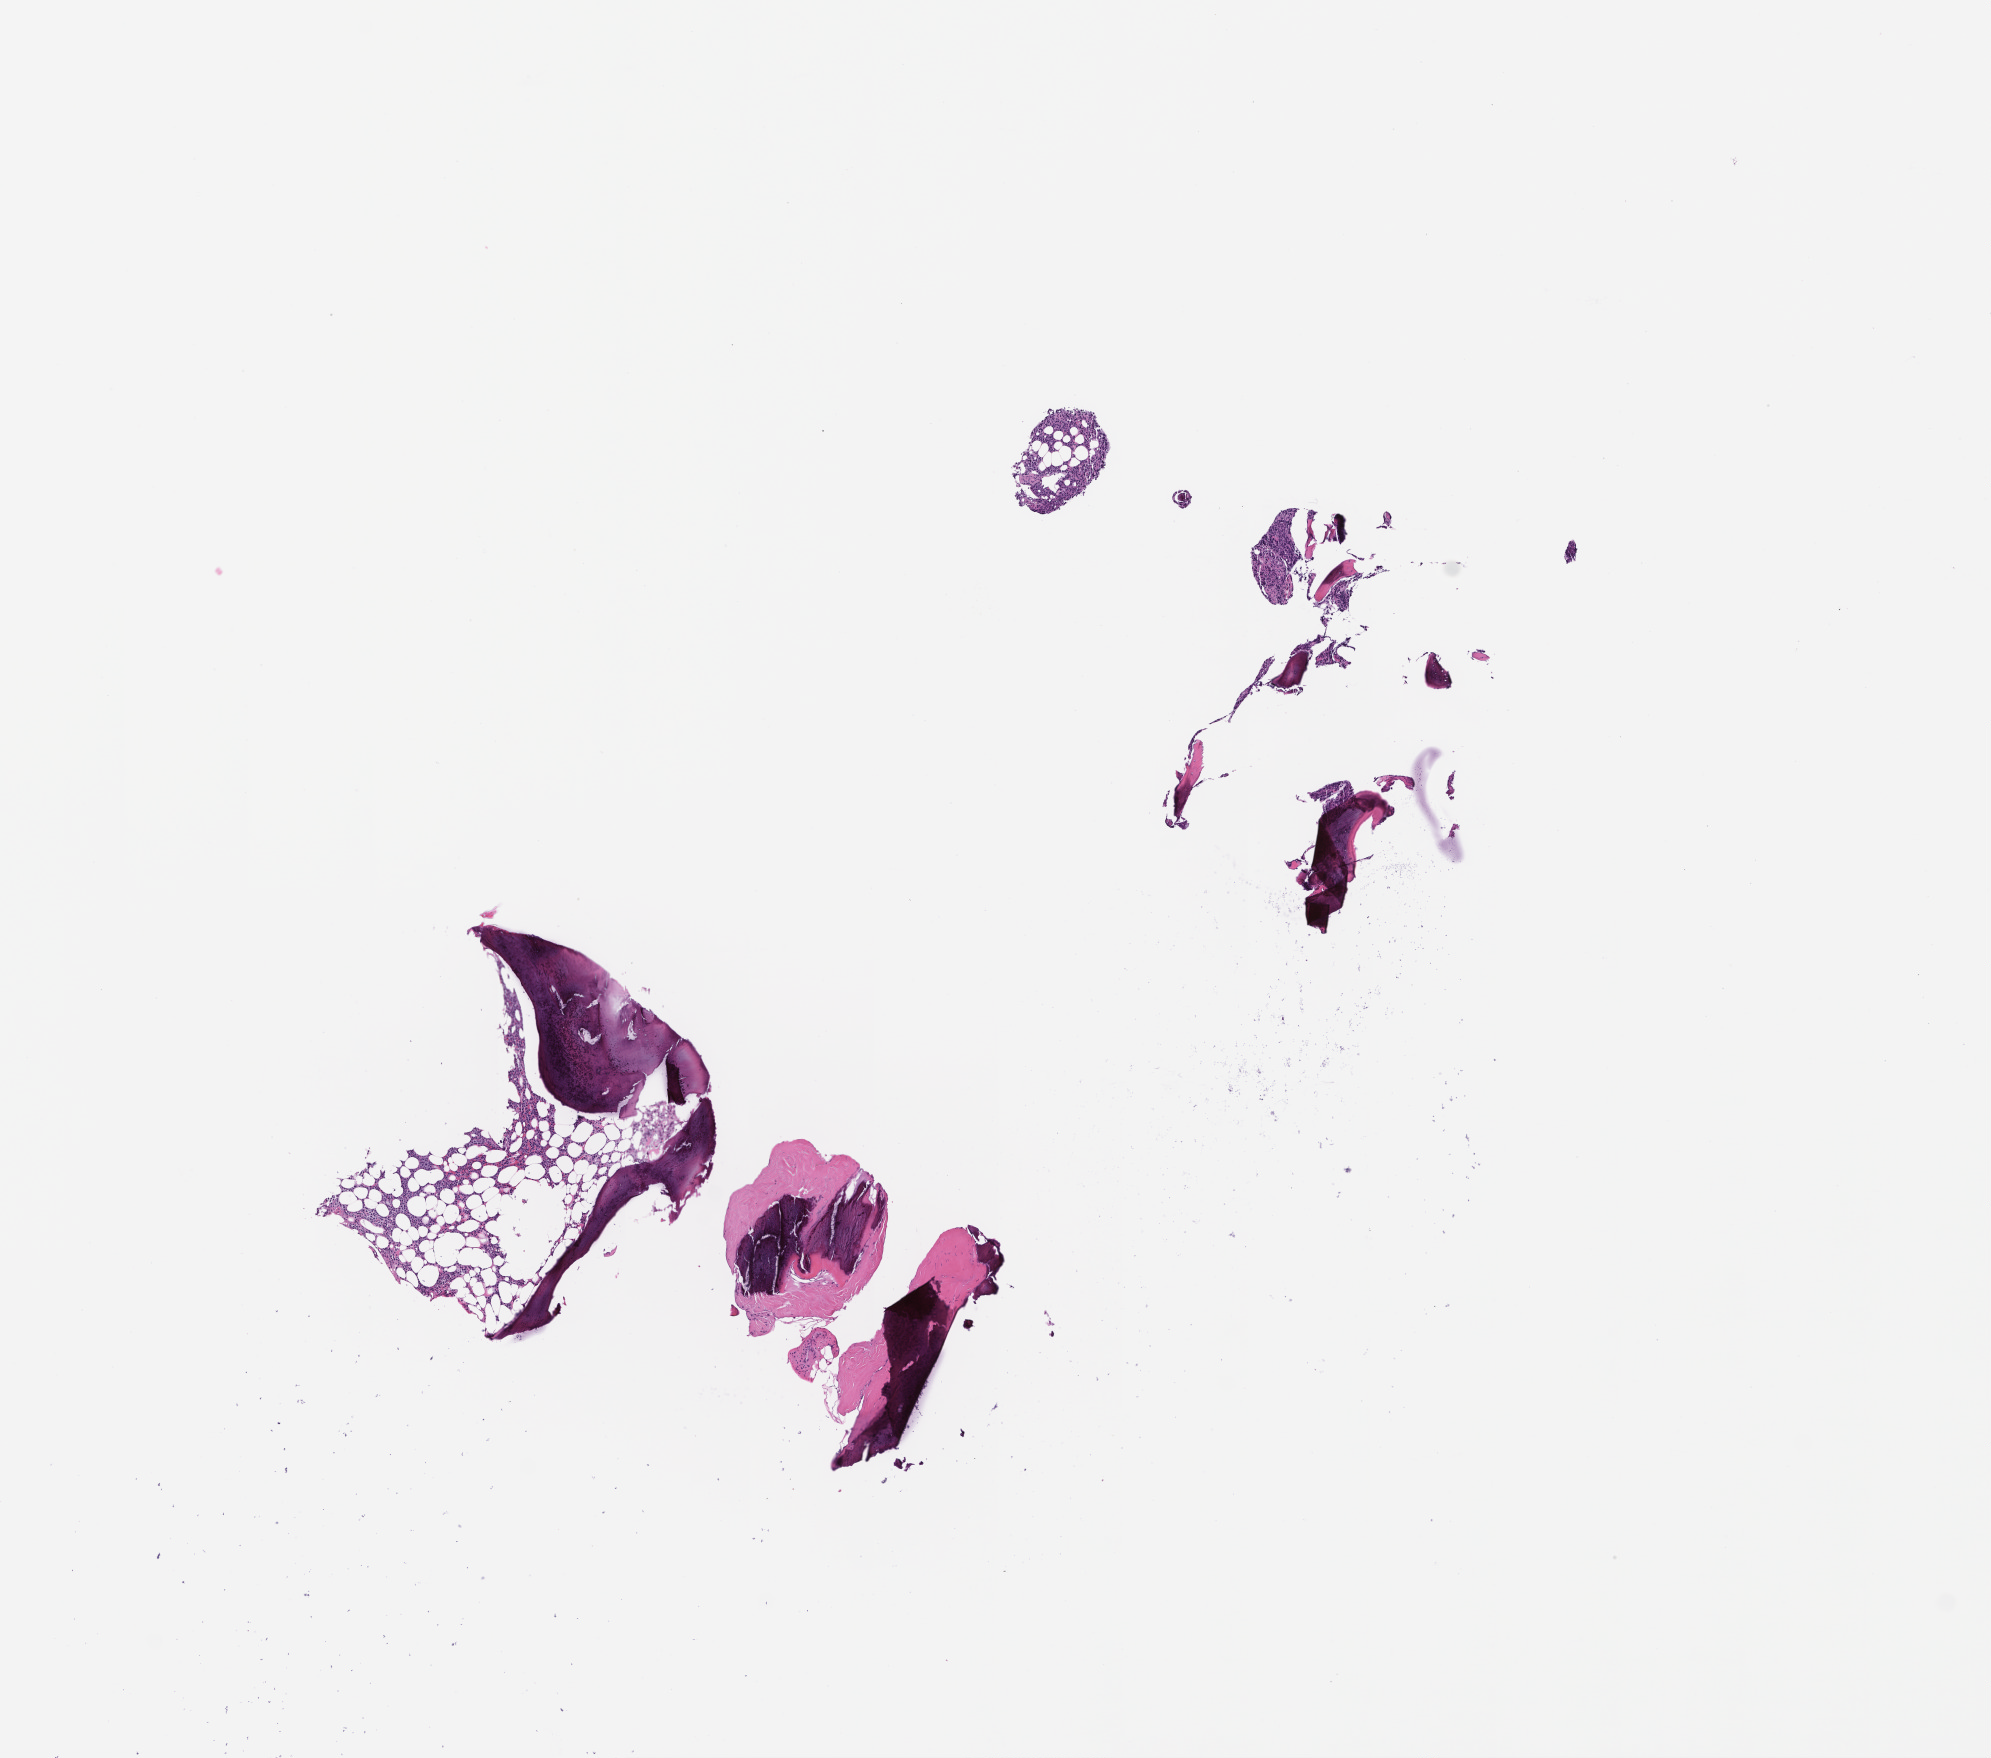
Whole-slide image, hematoxylin and eosin (H&E) stain, shown as a low-resolution overview of the whole scanned area (about 8.0 x 7.1 mm); FFPE section; tissue site: bone marrow; specimen time point: collected at baseline (before treatment). Patient: male.
This section: primary tumour tissue. Diagnosis: Plasma Cell Myeloma.